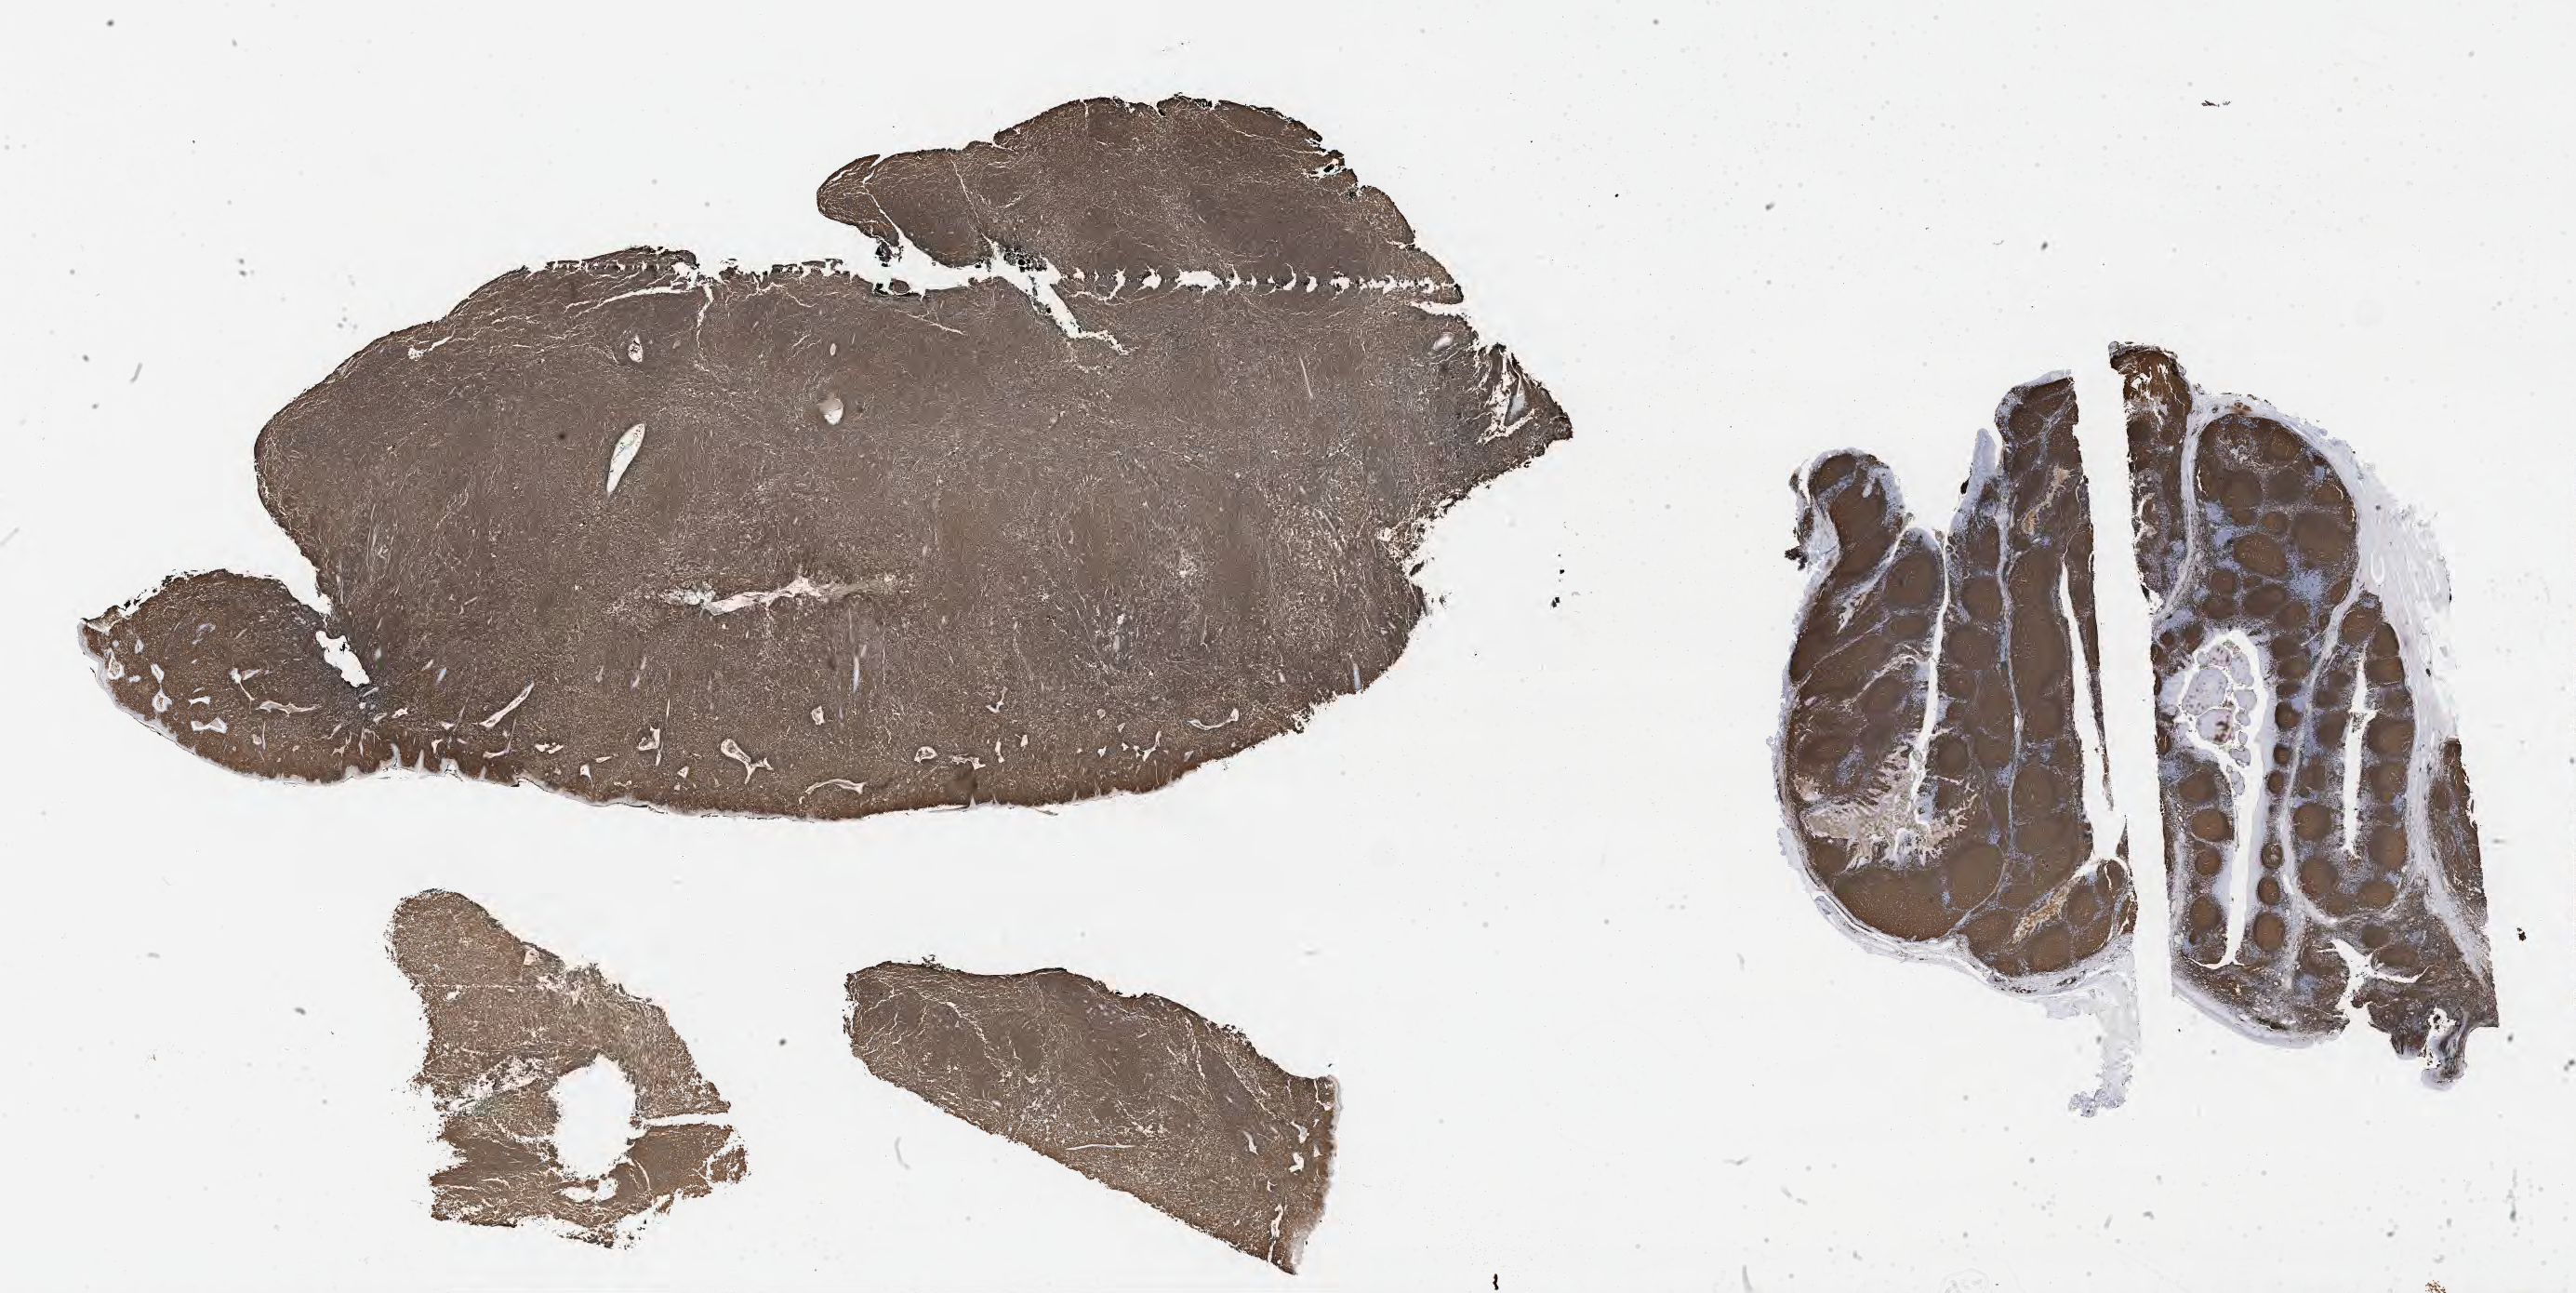
Whole-slide image, immunohistochemical stain for CD20 — shown as a low-resolution overview of the whole scanned area (about 44.8 x 22.5 mm), specimen: tumor tissue. Male patient, aged 46.
Diagnosis: Burkitt lymphoma, NOS.